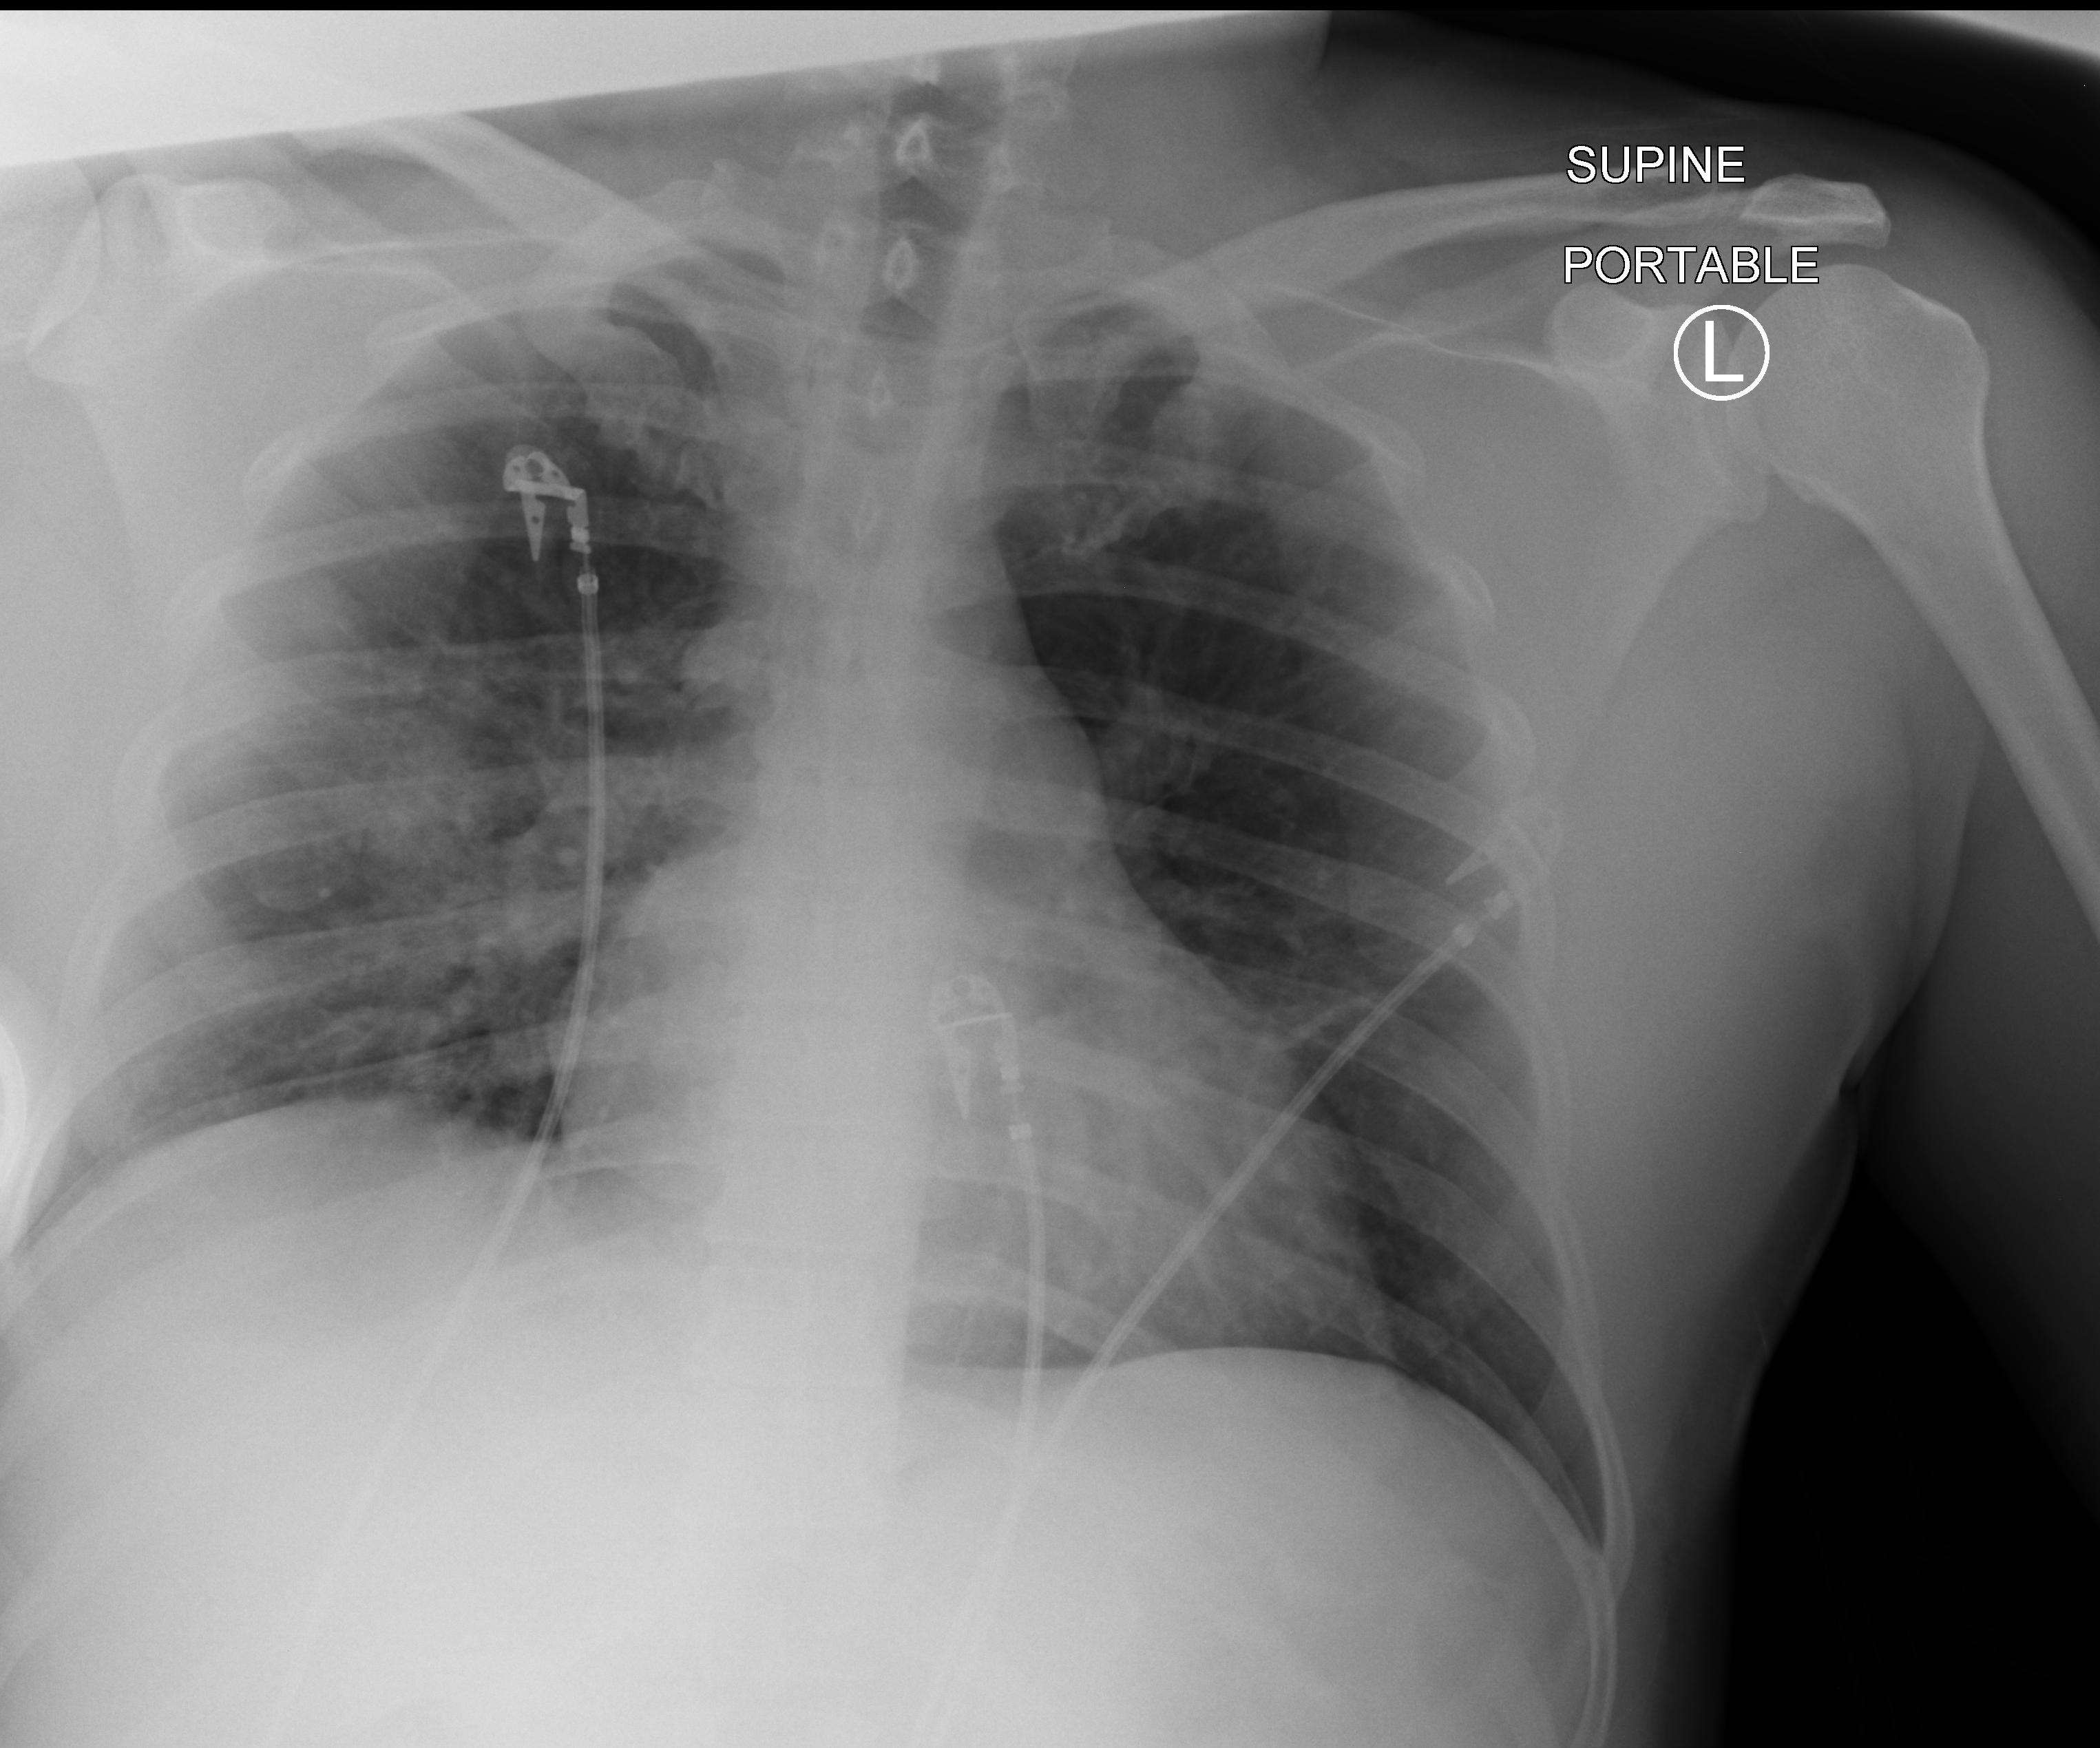
Bedside chest radiograph (computed radiography); anteroposterior (AP) projection. Male patient hospitalised with COVID-19, age 18–59 years.
Hospital-stay facts (about this admission, not read from this image; timing relative to this image not recorded): length of hospital stay: 10 days.